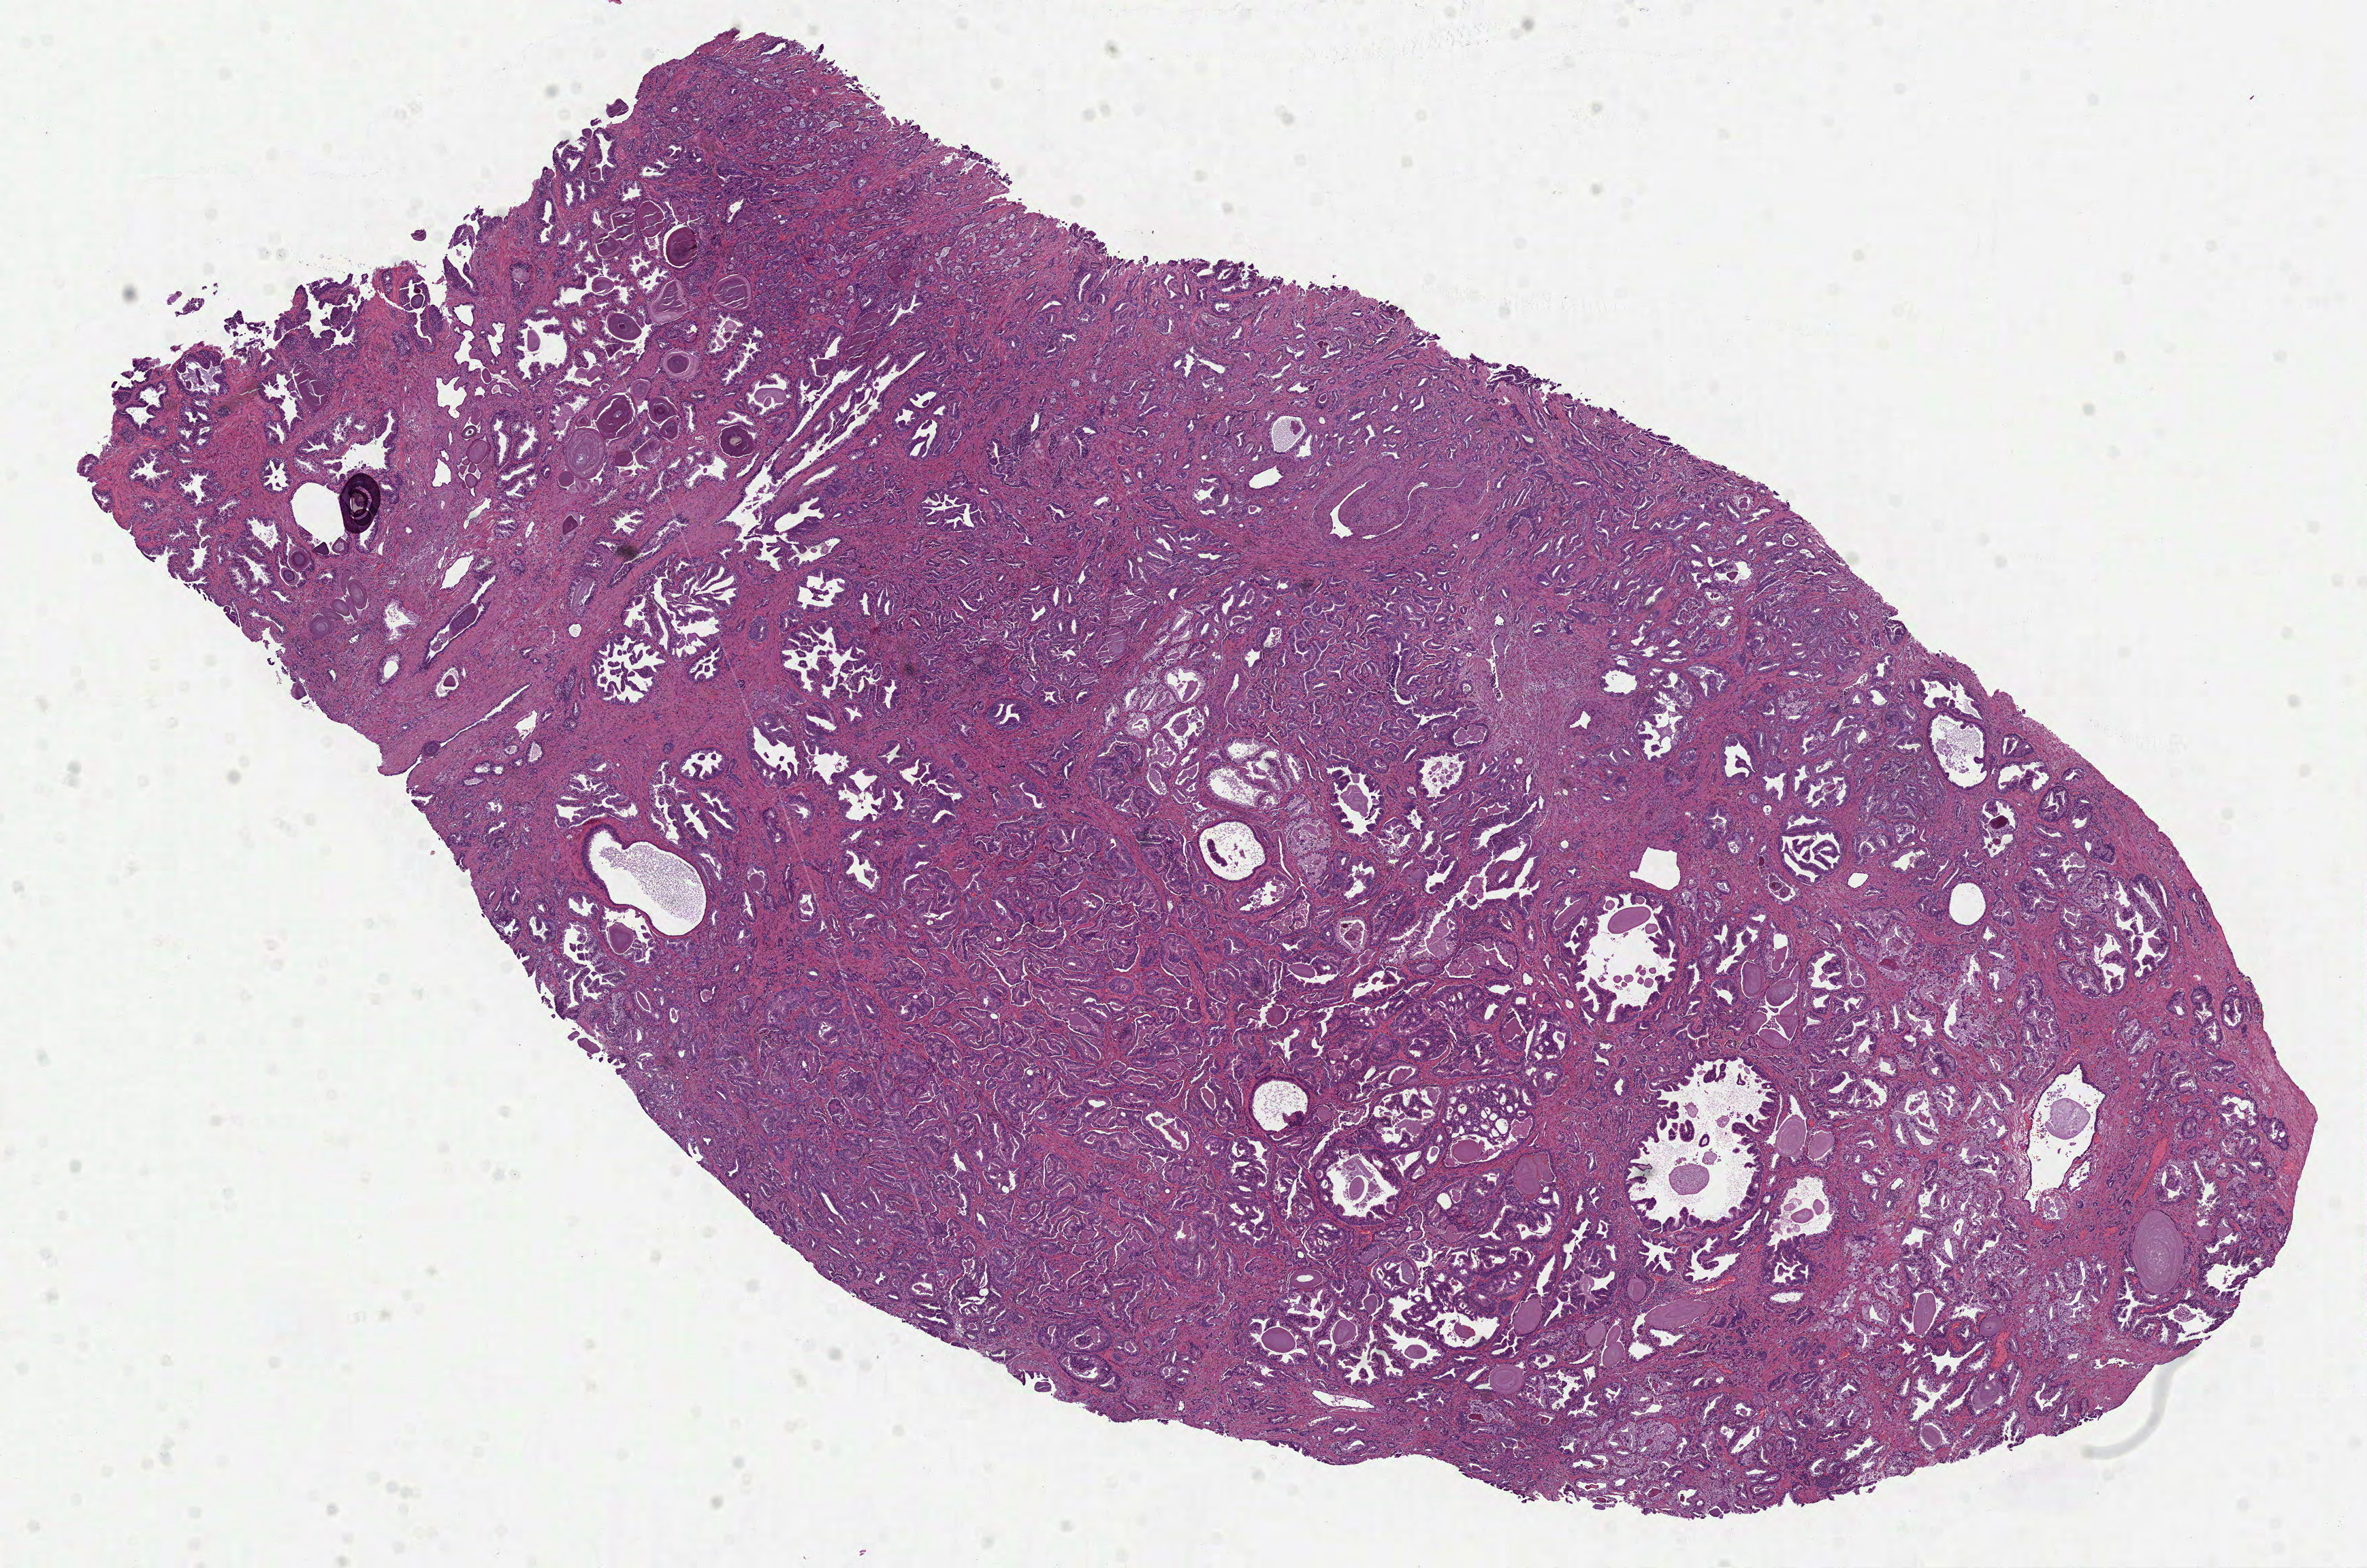
Hematoxylin and eosin (H&E) stained whole-slide image — whole scanned area (about 14.0 x 9.3 mm, acquisition: 40x scan) shown as a low-resolution overview; formalin-fixed paraffin-embedded (FFPE) diagnostic section; primary tumour sample from the prostate. Male patient; age at initial diagnosis 60 years. Gleason score: 6 (3+3).
• histologic diagnosis: Acinar cell carcinoma (prostate gland)
• laterality: right